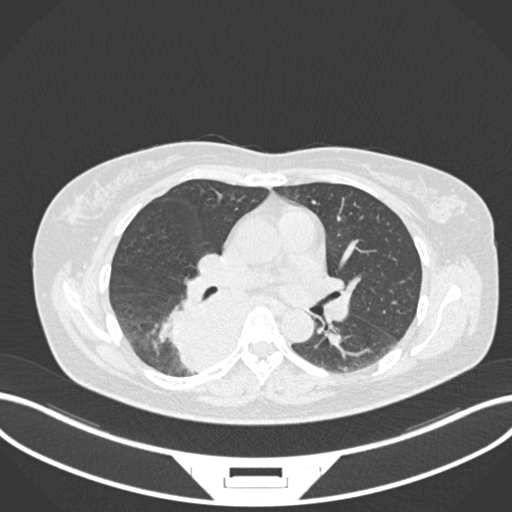
Chest CT, one axial slice; reconstruction kernel B30f; 120 kVp; lung window (W 1500 / L -600 HU); 1 mm slice thickness; 512 × 512 image matrix, field of view 400 × 400 mm. Patient: female, 54 years. From the clinical record (not read from this slice): clinical TNM (as recorded): T4 N0 M0.
Outlined on this slice (rectangle marked by the reading radiologist):
- lung tumour (recorded histology: adenocarcinoma): bounding box (x1, y1, x2, y2) in pixels: (168, 284, 256, 375)